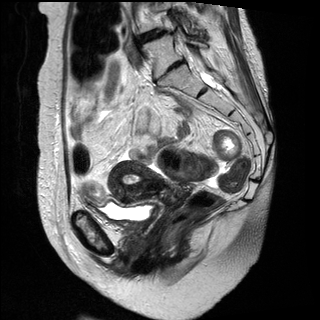
Pelvic MRI for cervical cancer, one sagittal slice. Slice 17 of 31 in the series (ordered by position). T2-weighted. 1.5 T. TE 89 ms, TR 3890 ms. 4 mm slice thickness. 320 × 320 image matrix, field of view 260 × 260 mm. Female patient, age 61 years.
Outlined on this slice (outlined manually by an expert reader):
- uterus and cervix: box from (x=107, y=158) to (x=194, y=209) px